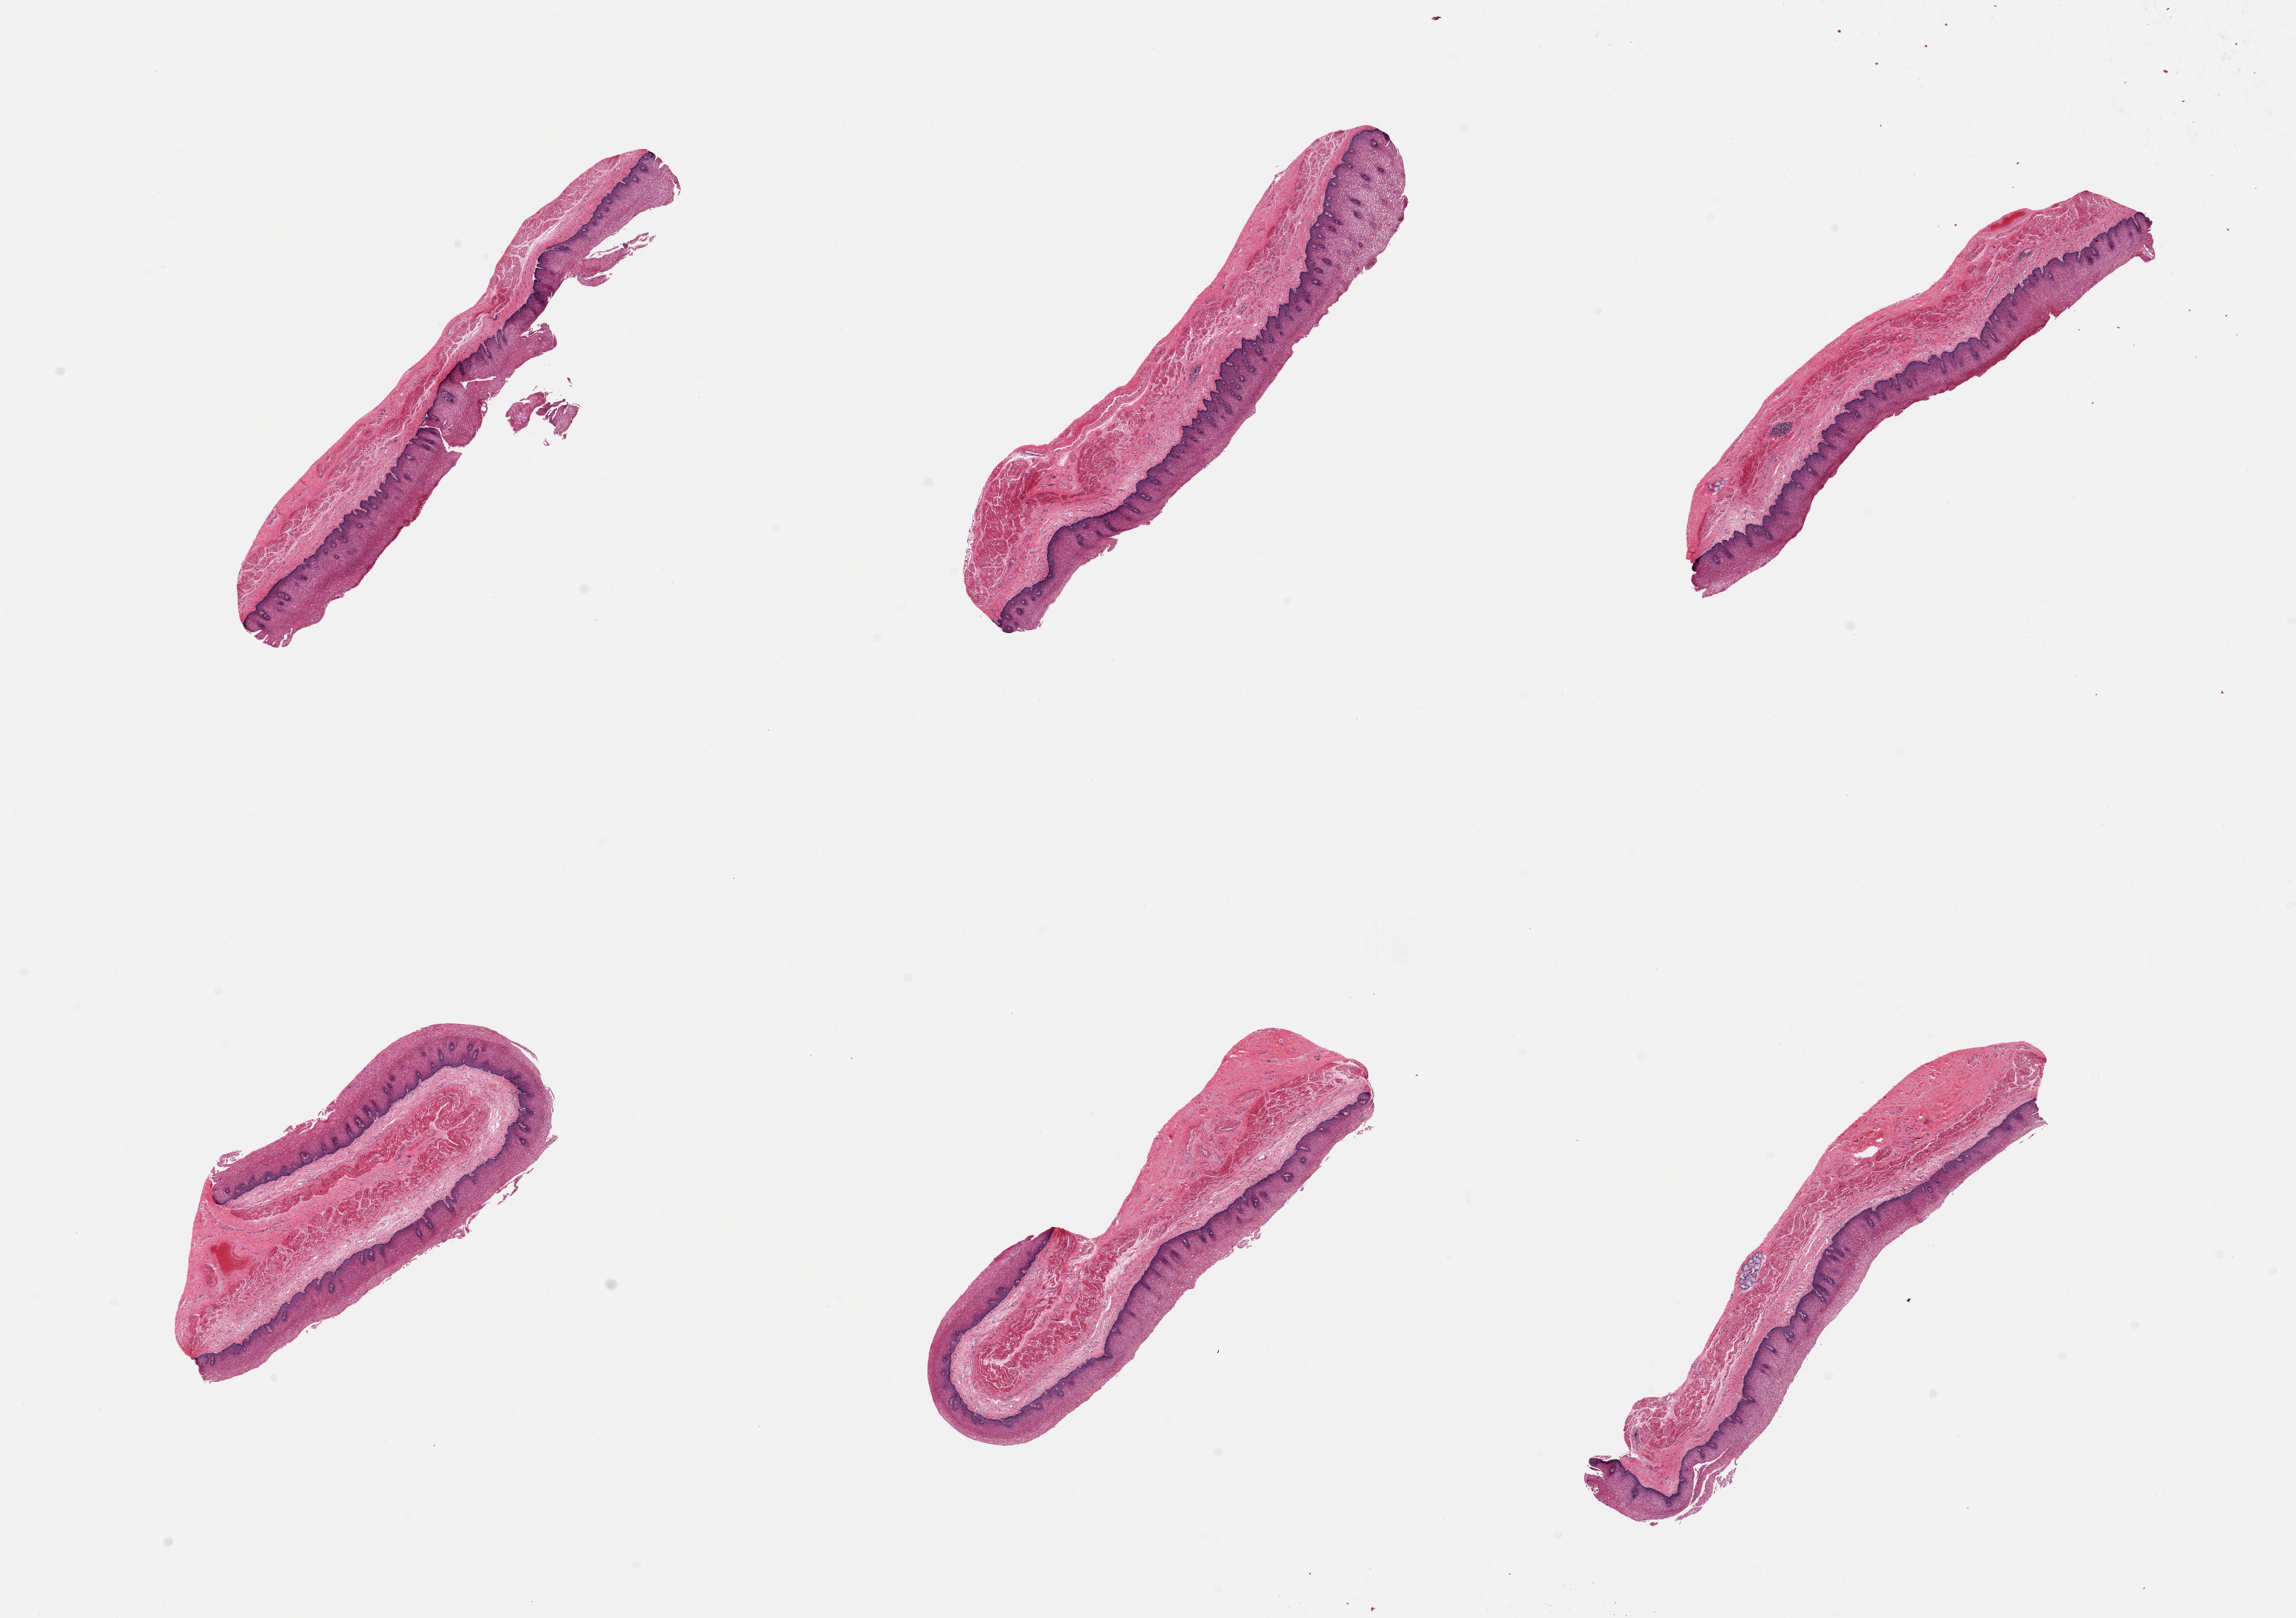
Digitized H&E-stained section, shown as a low-resolution overview of the whole scanned area (about 24.6 x 17.3 mm); PAXgene-fixed paraffin-embedded (PFPE) section; sampled site (target tissue): esophageal mucous membrane; tissue donor sample. Donor: male.
Pathologist's review note for this sample: 6 pieces, squamous mucosa ~0.5mm, ~ 50% thickness; Incidental submucosal mucus gland.